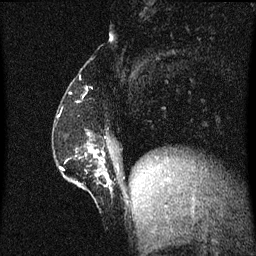
Breast MRI (dynamic contrast-enhanced), one sagittal slice; slice 16 of 60 in the series (ordered by position); dynamic contrast-enhanced series, image 2 of 3 at this slice position (ordered by acquisition); 1.5 T; TE 4.2 ms, TR 8.4 ms; 2 mm slice thickness; 256 × 256 image matrix, field of view 200 × 200 mm. Female patient, age 52 years. From the clinical record (not read from this slice): setting: breast cancer imaged before/during neoadjuvant chemotherapy; receptor status: HER2-positive.
Structures marked on this image (semi-automatic segmentation, software-assisted and operator-edited):
- analysis volume of interest (the breast-tissue region the enhancement analysis was run in; not a lesion): bounding box (x1, y1, x2, y2) in pixels: (62, 132, 116, 199)
- tumour enhancement mask (voxels above the 70 % enhancement threshold inside the analysis volume of interest): (89, 148, 110, 181)